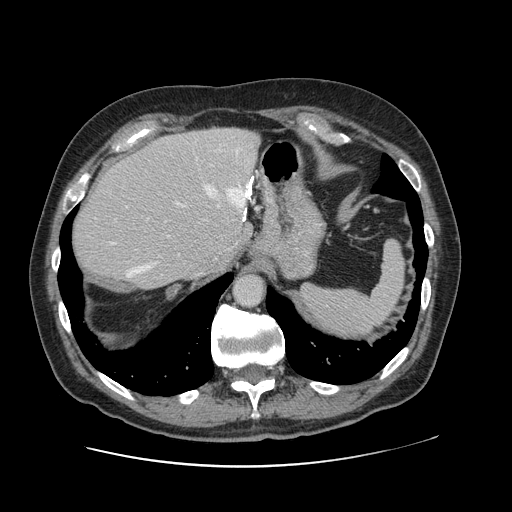
Contrast-enhanced abdominal CT, one axial slice. Slice 91 of 138 in the series (ordered by position). Intravenous contrast given. Soft-tissue window (W 400 / L 40 HU). 2.5 mm slice thickness. 512 × 512 image matrix. Male patient, age 71 years. From the clinical record (not read from this slice): diagnosis: colorectal cancer liver metastases, imaged before liver resection; multiple liver metastases: no; largest metastasis: 3.3 cm; chemotherapy before resection: no.
Annotated regions visible in this slice (manually delineated by an expert):
- hepatic veins: box from (x=127, y=177) to (x=253, y=277) px
- liver: (x=72, y=128)–(x=259, y=289)
- planned liver remnant (the part of the liver to remain after resection): (x=72, y=155)–(x=241, y=289)
- portal vein (with intrahepatic branches): (x=110, y=201)–(x=186, y=245)